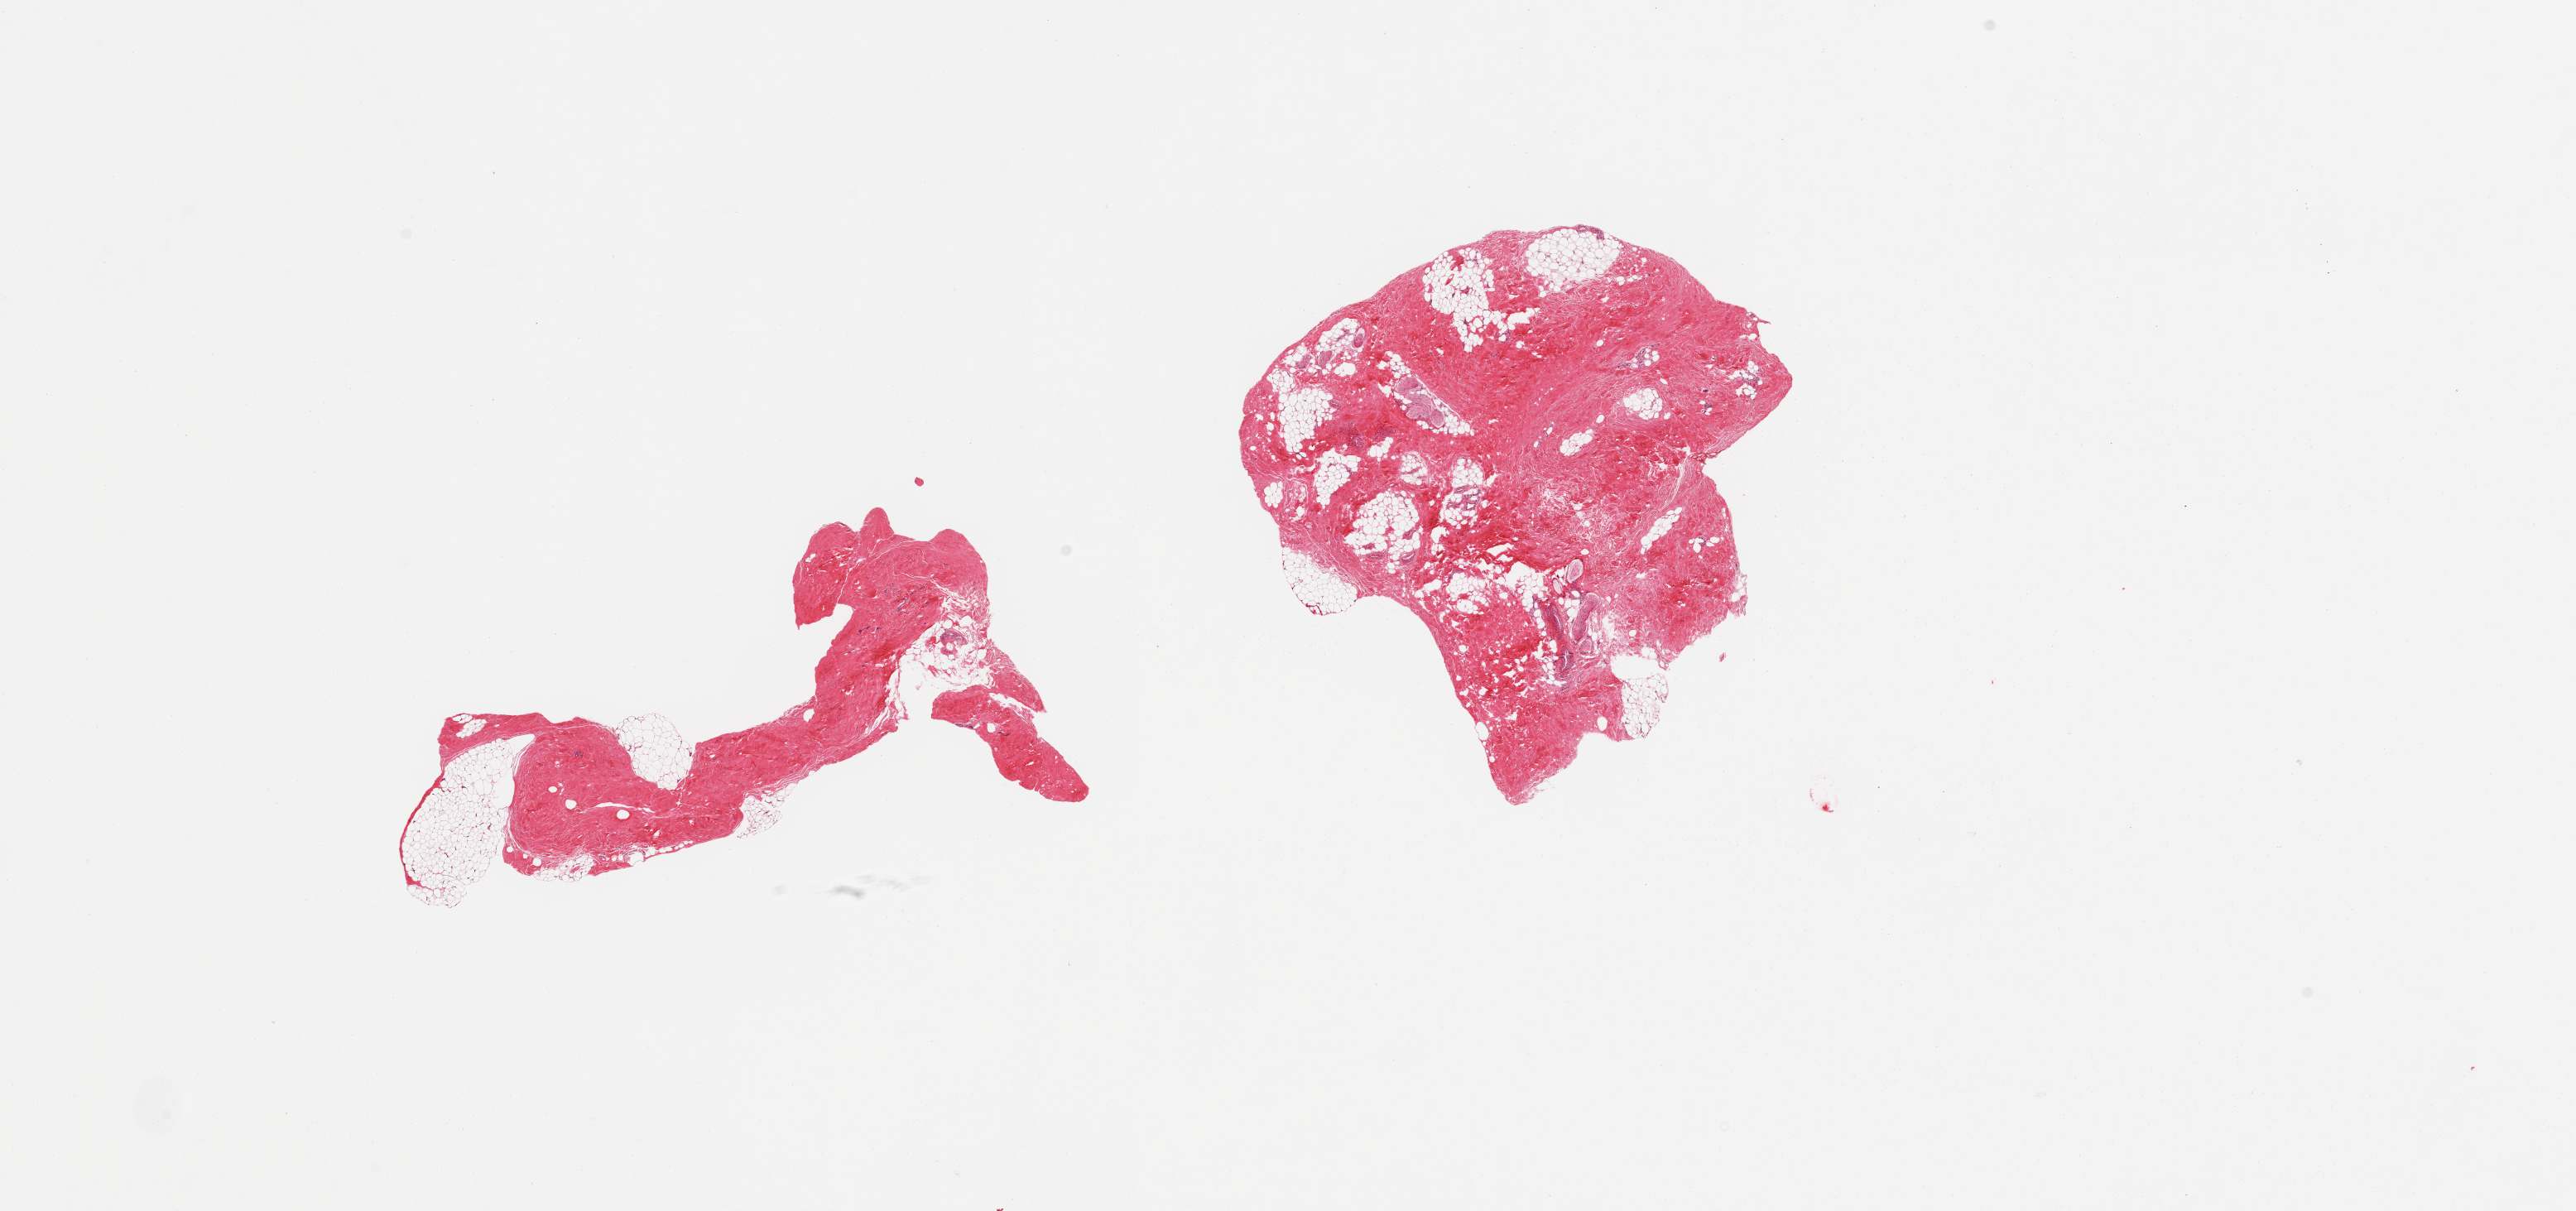
Digitized H&E-stained section, brightfield — a low-resolution overview of the entire scanned area, about 24.6 x 11.6 mm, PAXgene-fixed paraffin-embedded (PFPE) section, sampled site (target tissue): breast, donor tissue sample. Donor sex: male.
Pathologist's review note for this sample: 2 pieces, gynecomastoid stromal hyperplasia; no ductal elements but a few incidental peripheral nerve elements noted.